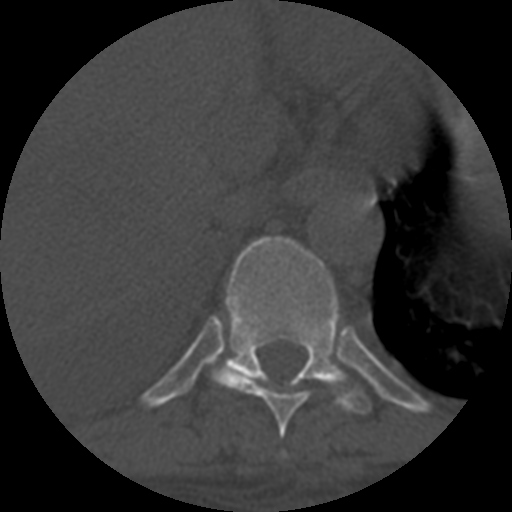
CT including the spine, one axial slice. Position 366 of 708 along the scan axis. Reconstruction kernel STANDARD. 120 kVp. One of 3 acquisitions stored at this slice position. Bone window (W 1800 / L 400 HU). 512 × 512 image matrix, field of view 160 × 160 mm. Patient age 55 years. Case-level facts recorded for this patient, not image findings: primary cancer: colon; vertebrae with lytic lesions (as recorded): T12, L1, L5.
Structures marked on this image (semi-automatic segmentation, software-assisted and operator-edited):
- T10 vertebra: box from (x=223, y=237) to (x=372, y=414) px
- T9 vertebra: (x=211, y=366)–(x=310, y=437)